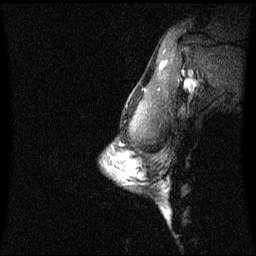
Breast MRI (dynamic contrast-enhanced), one sagittal slice; dynamic contrast-enhanced series, image 2 of 3 at this slice position (ordered by acquisition); 1.5 T; TE 4.2 ms, TR 8.4 ms; 256 × 256 image matrix, field of view 240 × 240 mm. Female patient, age 42 years. From the clinical record (not read from this slice): setting: breast cancer imaged before/during neoadjuvant chemotherapy; receptor status: triple-negative.
Structures marked on this image (semi-automatically segmented with operator editing):
- analysis volume of interest (the breast-tissue region the enhancement analysis was run in; not a lesion): bounding box <106,156,137,181> (left, top, right, bottom; pixels)
- tumour enhancement mask (voxels above the 70 % enhancement threshold inside the analysis volume of interest): <113,156,136,175>